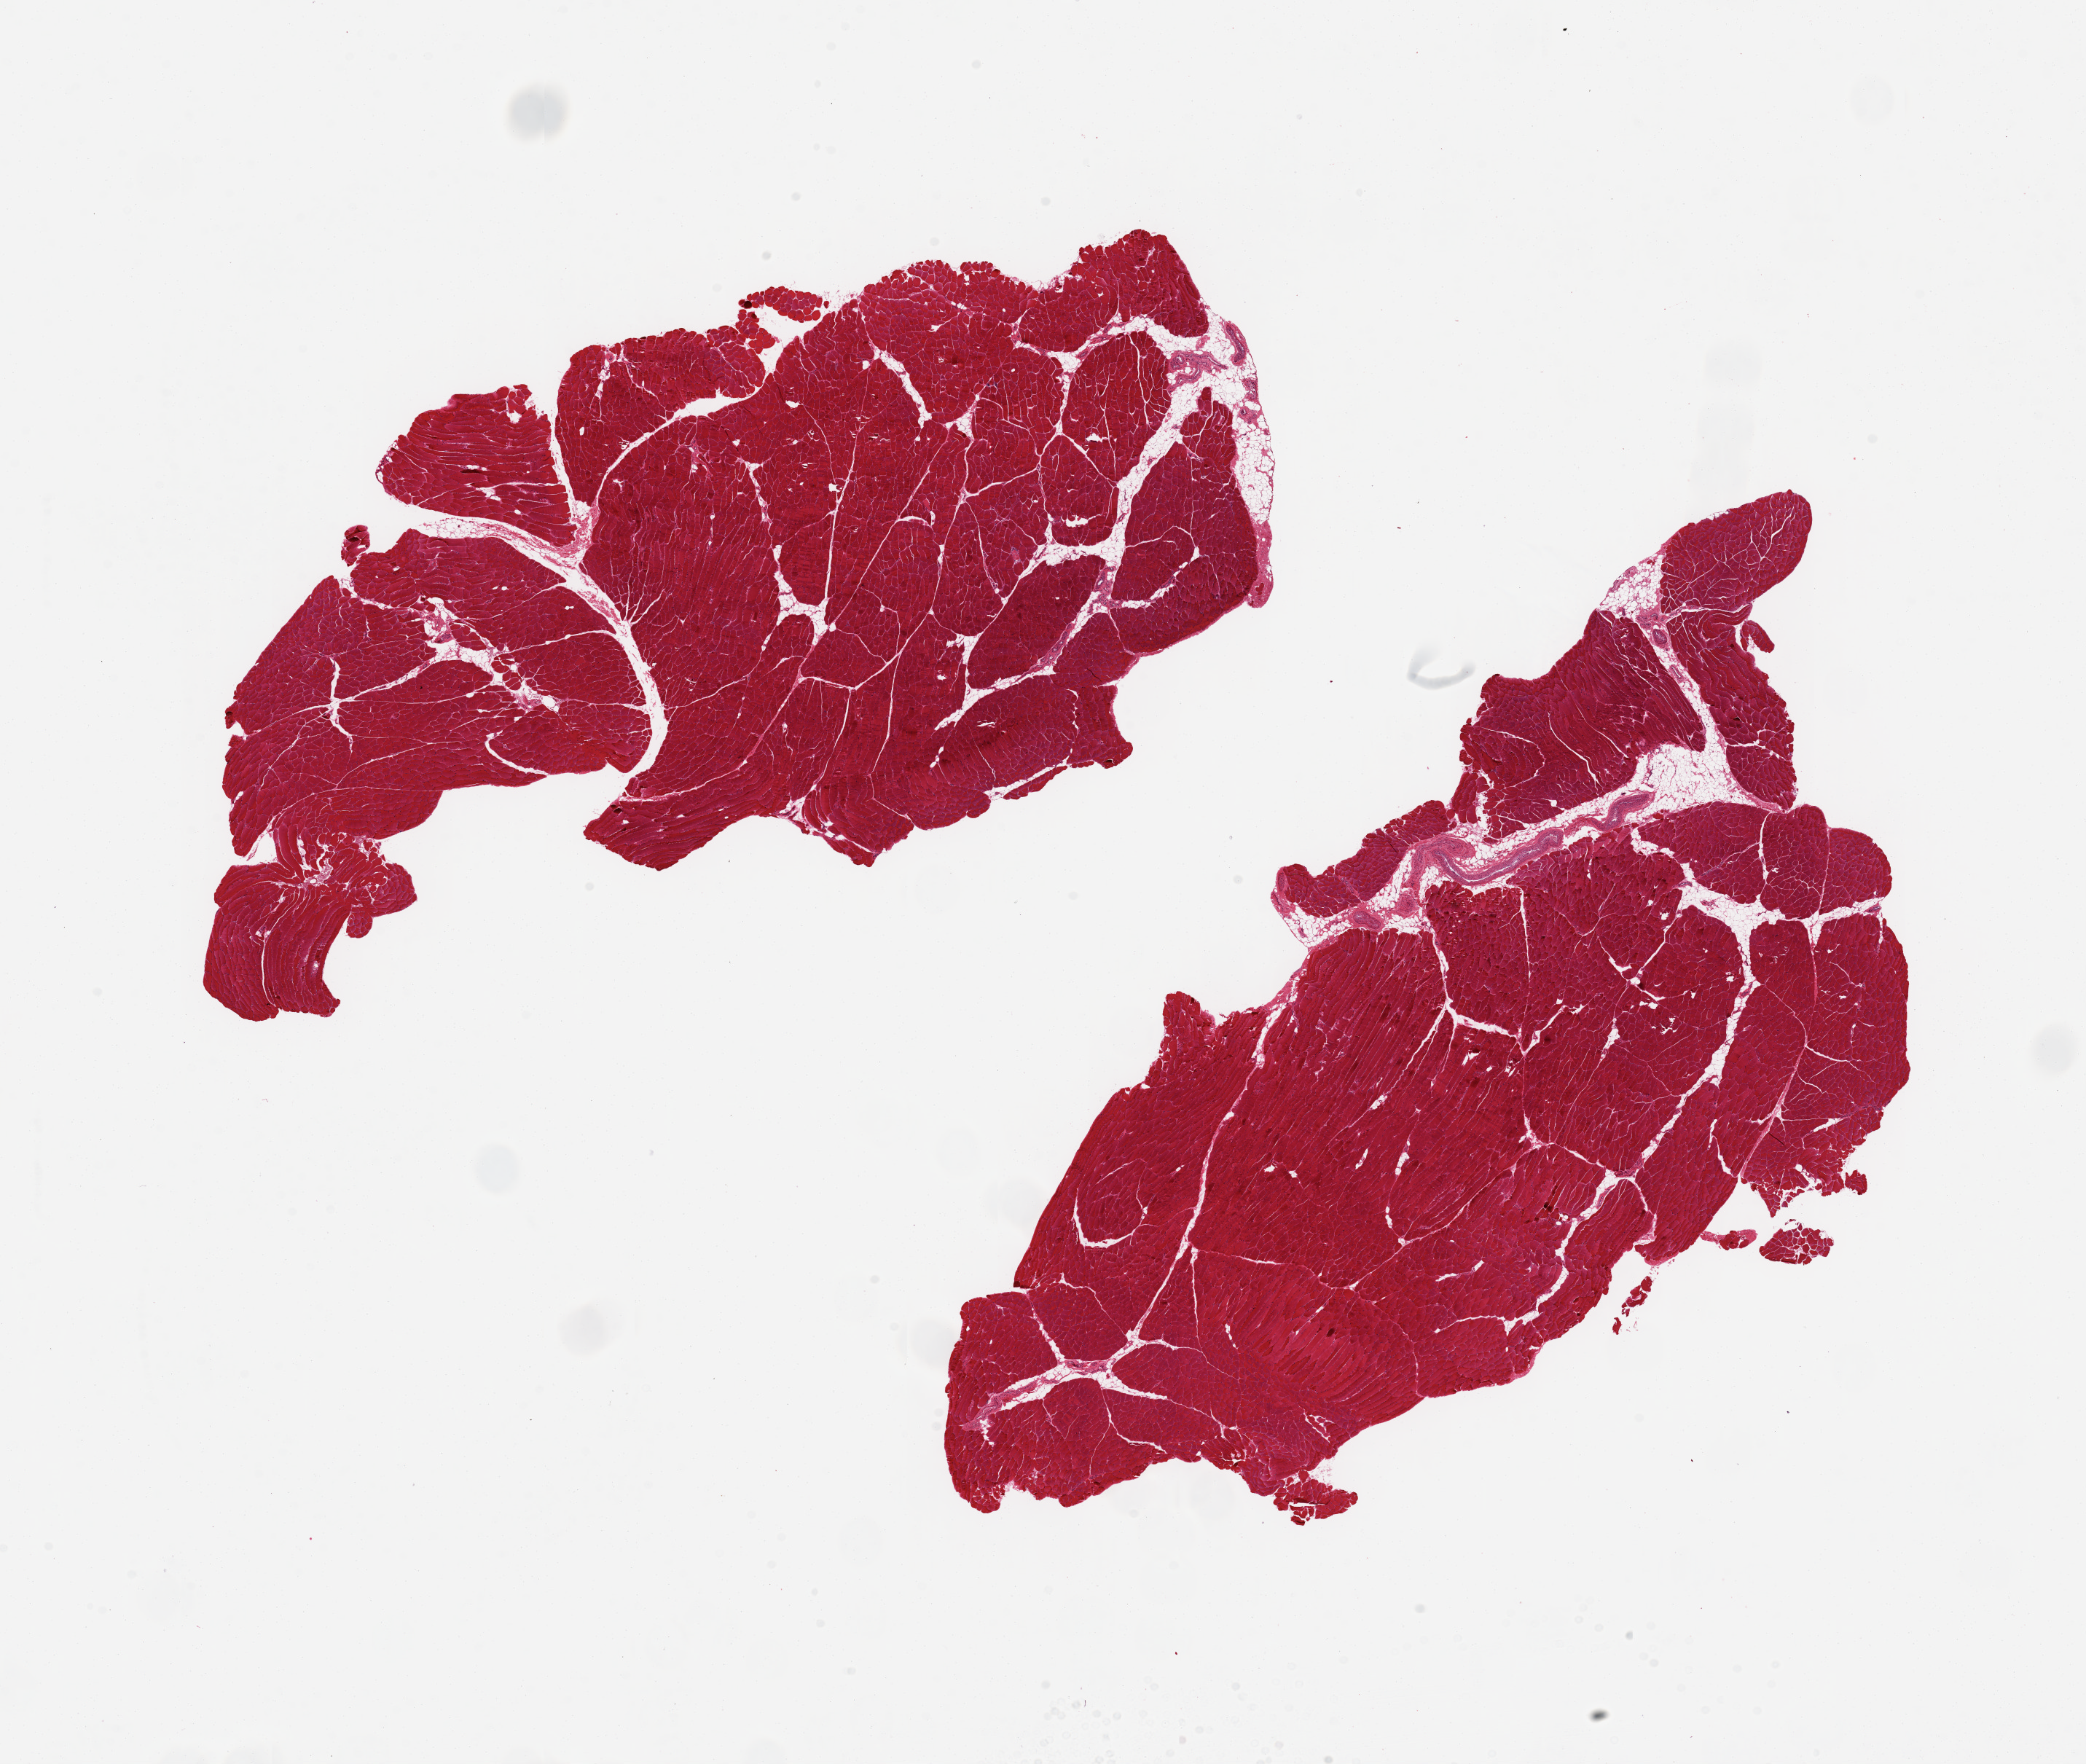
Digitized haematoxylin and eosin-stained section — a low-resolution overview of the entire scanned area, about 22.6 x 19.1 mm (from a 20x scan). PAXgene-fixed, paraffin-embedded tissue. Sampled site (target tissue): skeletal muscle. Donor tissue sample. Female donor.
Reviewer comment on this tissue sample: 2 aliquots, ~11x6mm. Minimal fat.